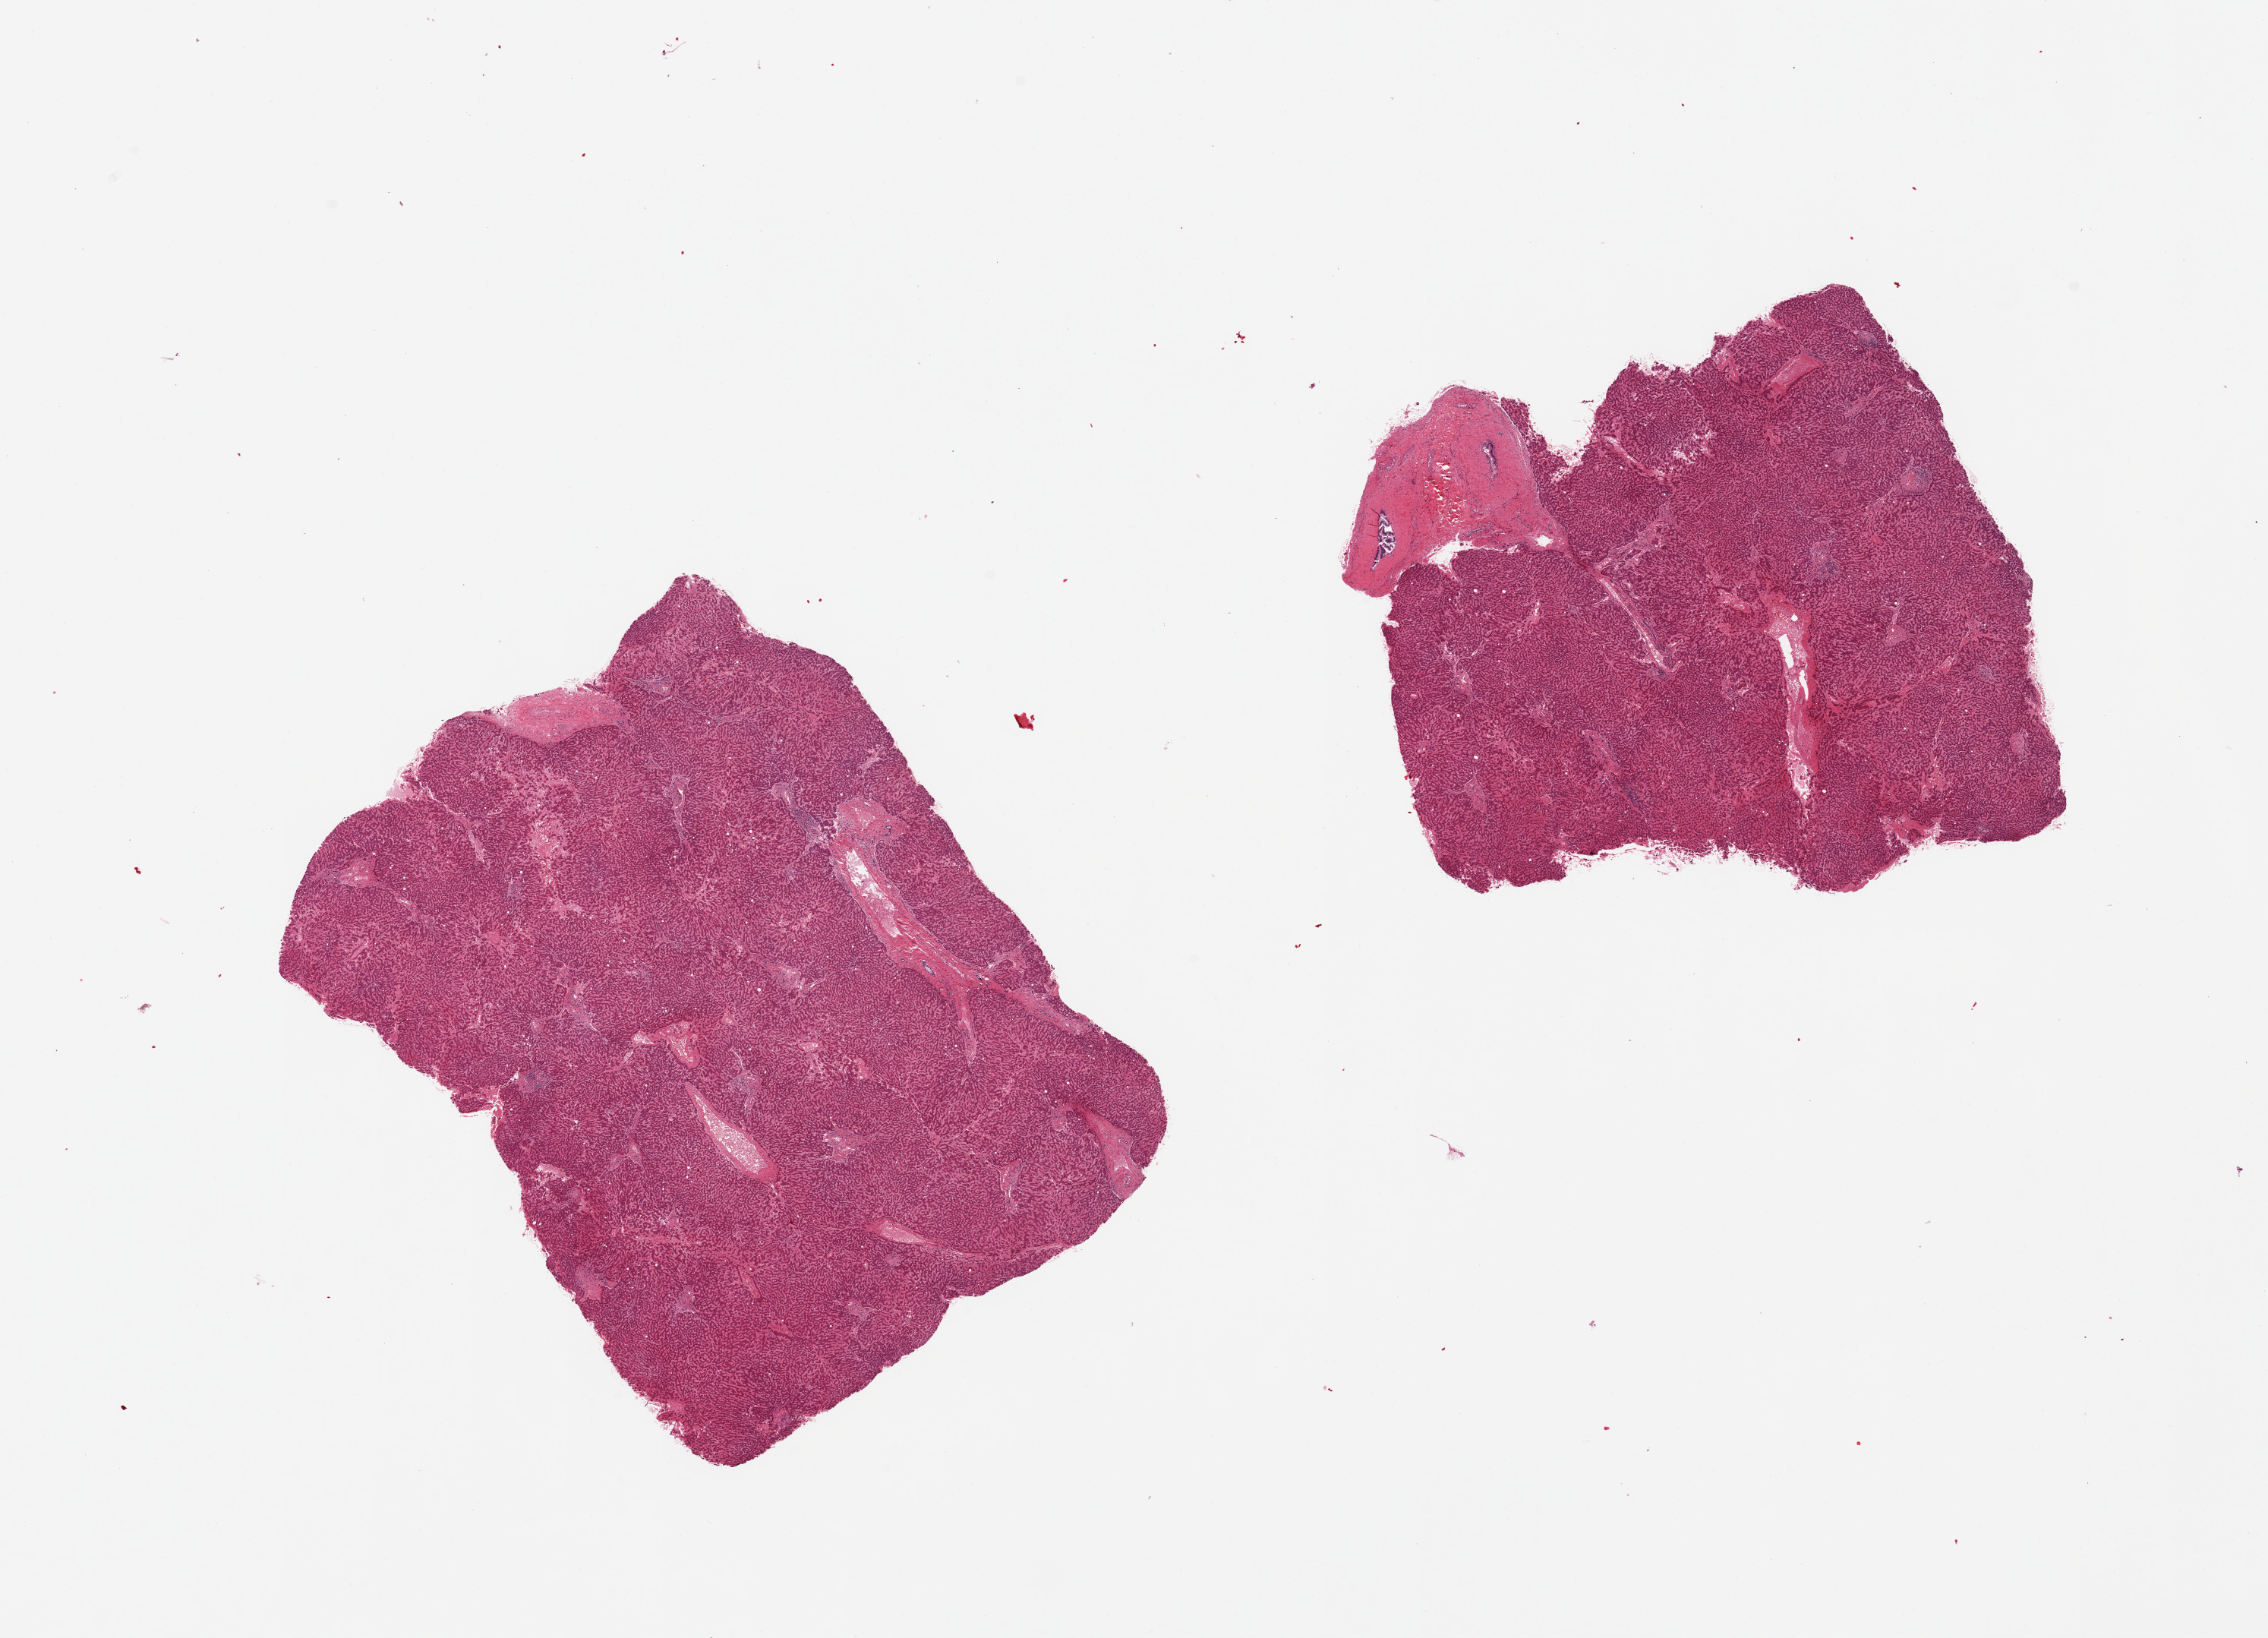
Digitized hematoxylin and eosin (H&E)-stained section — shown as a low-resolution overview of the whole scanned area (about 23.6 x 17.1 mm); PAXgene-fixed, paraffin-embedded tissue; sampled site (target tissue): liver; donor tissue sample. Female donor.
Review note (as recorded): 2 pieces, some foci more autolyzed, approach score 2; minimal steatosis.